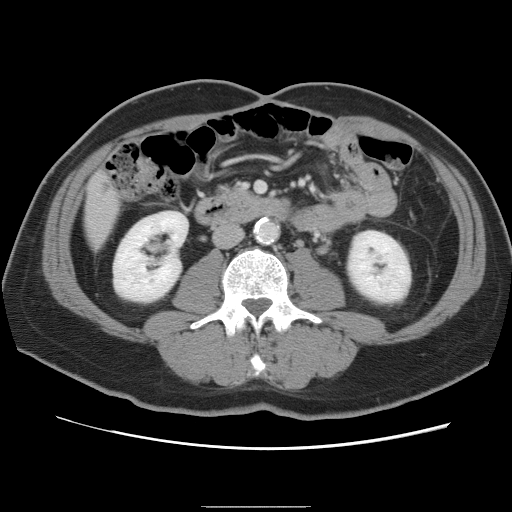
Contrast-enhanced abdominal CT, one axial slice; position 19 of 87 along the scan axis; 120 kVp; intravenous contrast given; soft-tissue window (W 400 / L 40 HU); 512 × 512 image matrix. Male patient, age 63 years. From the clinical record (not read from this slice): diagnosis: colorectal cancer liver metastases, imaged before liver resection; multiple liver metastases: no; largest metastasis: 9 cm; disease in both lobes: no.
Outlined on this slice (outlined manually by an expert reader):
- liver: bounding box [x1, y1, x2, y2] px = [85, 172, 120, 245]
- planned liver remnant (the part of the liver to remain after resection): [85, 172, 121, 245]
- liver metastasis: [104, 183, 110, 191]